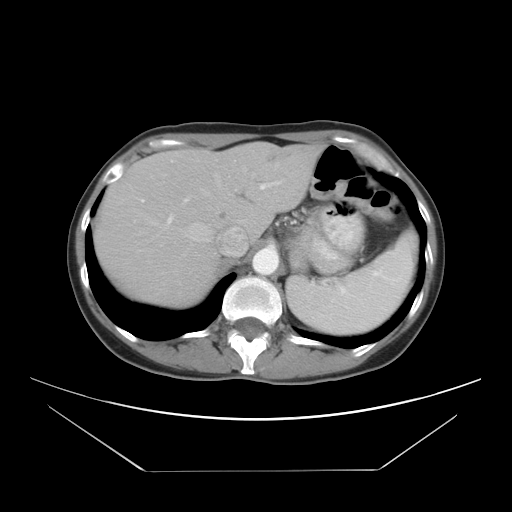
Contrast-enhanced abdominal CT, one axial slice. Position 22 of 30 along the scan axis. 120 kVp. Intravenous contrast given. Soft-tissue window (W 400 / L 40 HU). 7.5 mm slice thickness. 512 × 512 image matrix, field of view 412 × 412 mm. Female patient, age 54 years. Case-level facts recorded for this patient, not image findings: diagnosis: colorectal cancer liver metastases, imaged before liver resection; multiple liver metastases: yes; largest metastasis: 2.5 cm.
Outlined on this slice (expert manual segmentation):
- hepatic veins: bounding box [x1, y1, x2, y2] px = [137, 174, 244, 252]
- liver: [96, 144, 320, 304]
- planned liver remnant (the part of the liver to remain after resection): [96, 148, 270, 304]
- portal vein (with intrahepatic branches): [153, 182, 280, 239]
- liver metastasis: [267, 153, 283, 164]